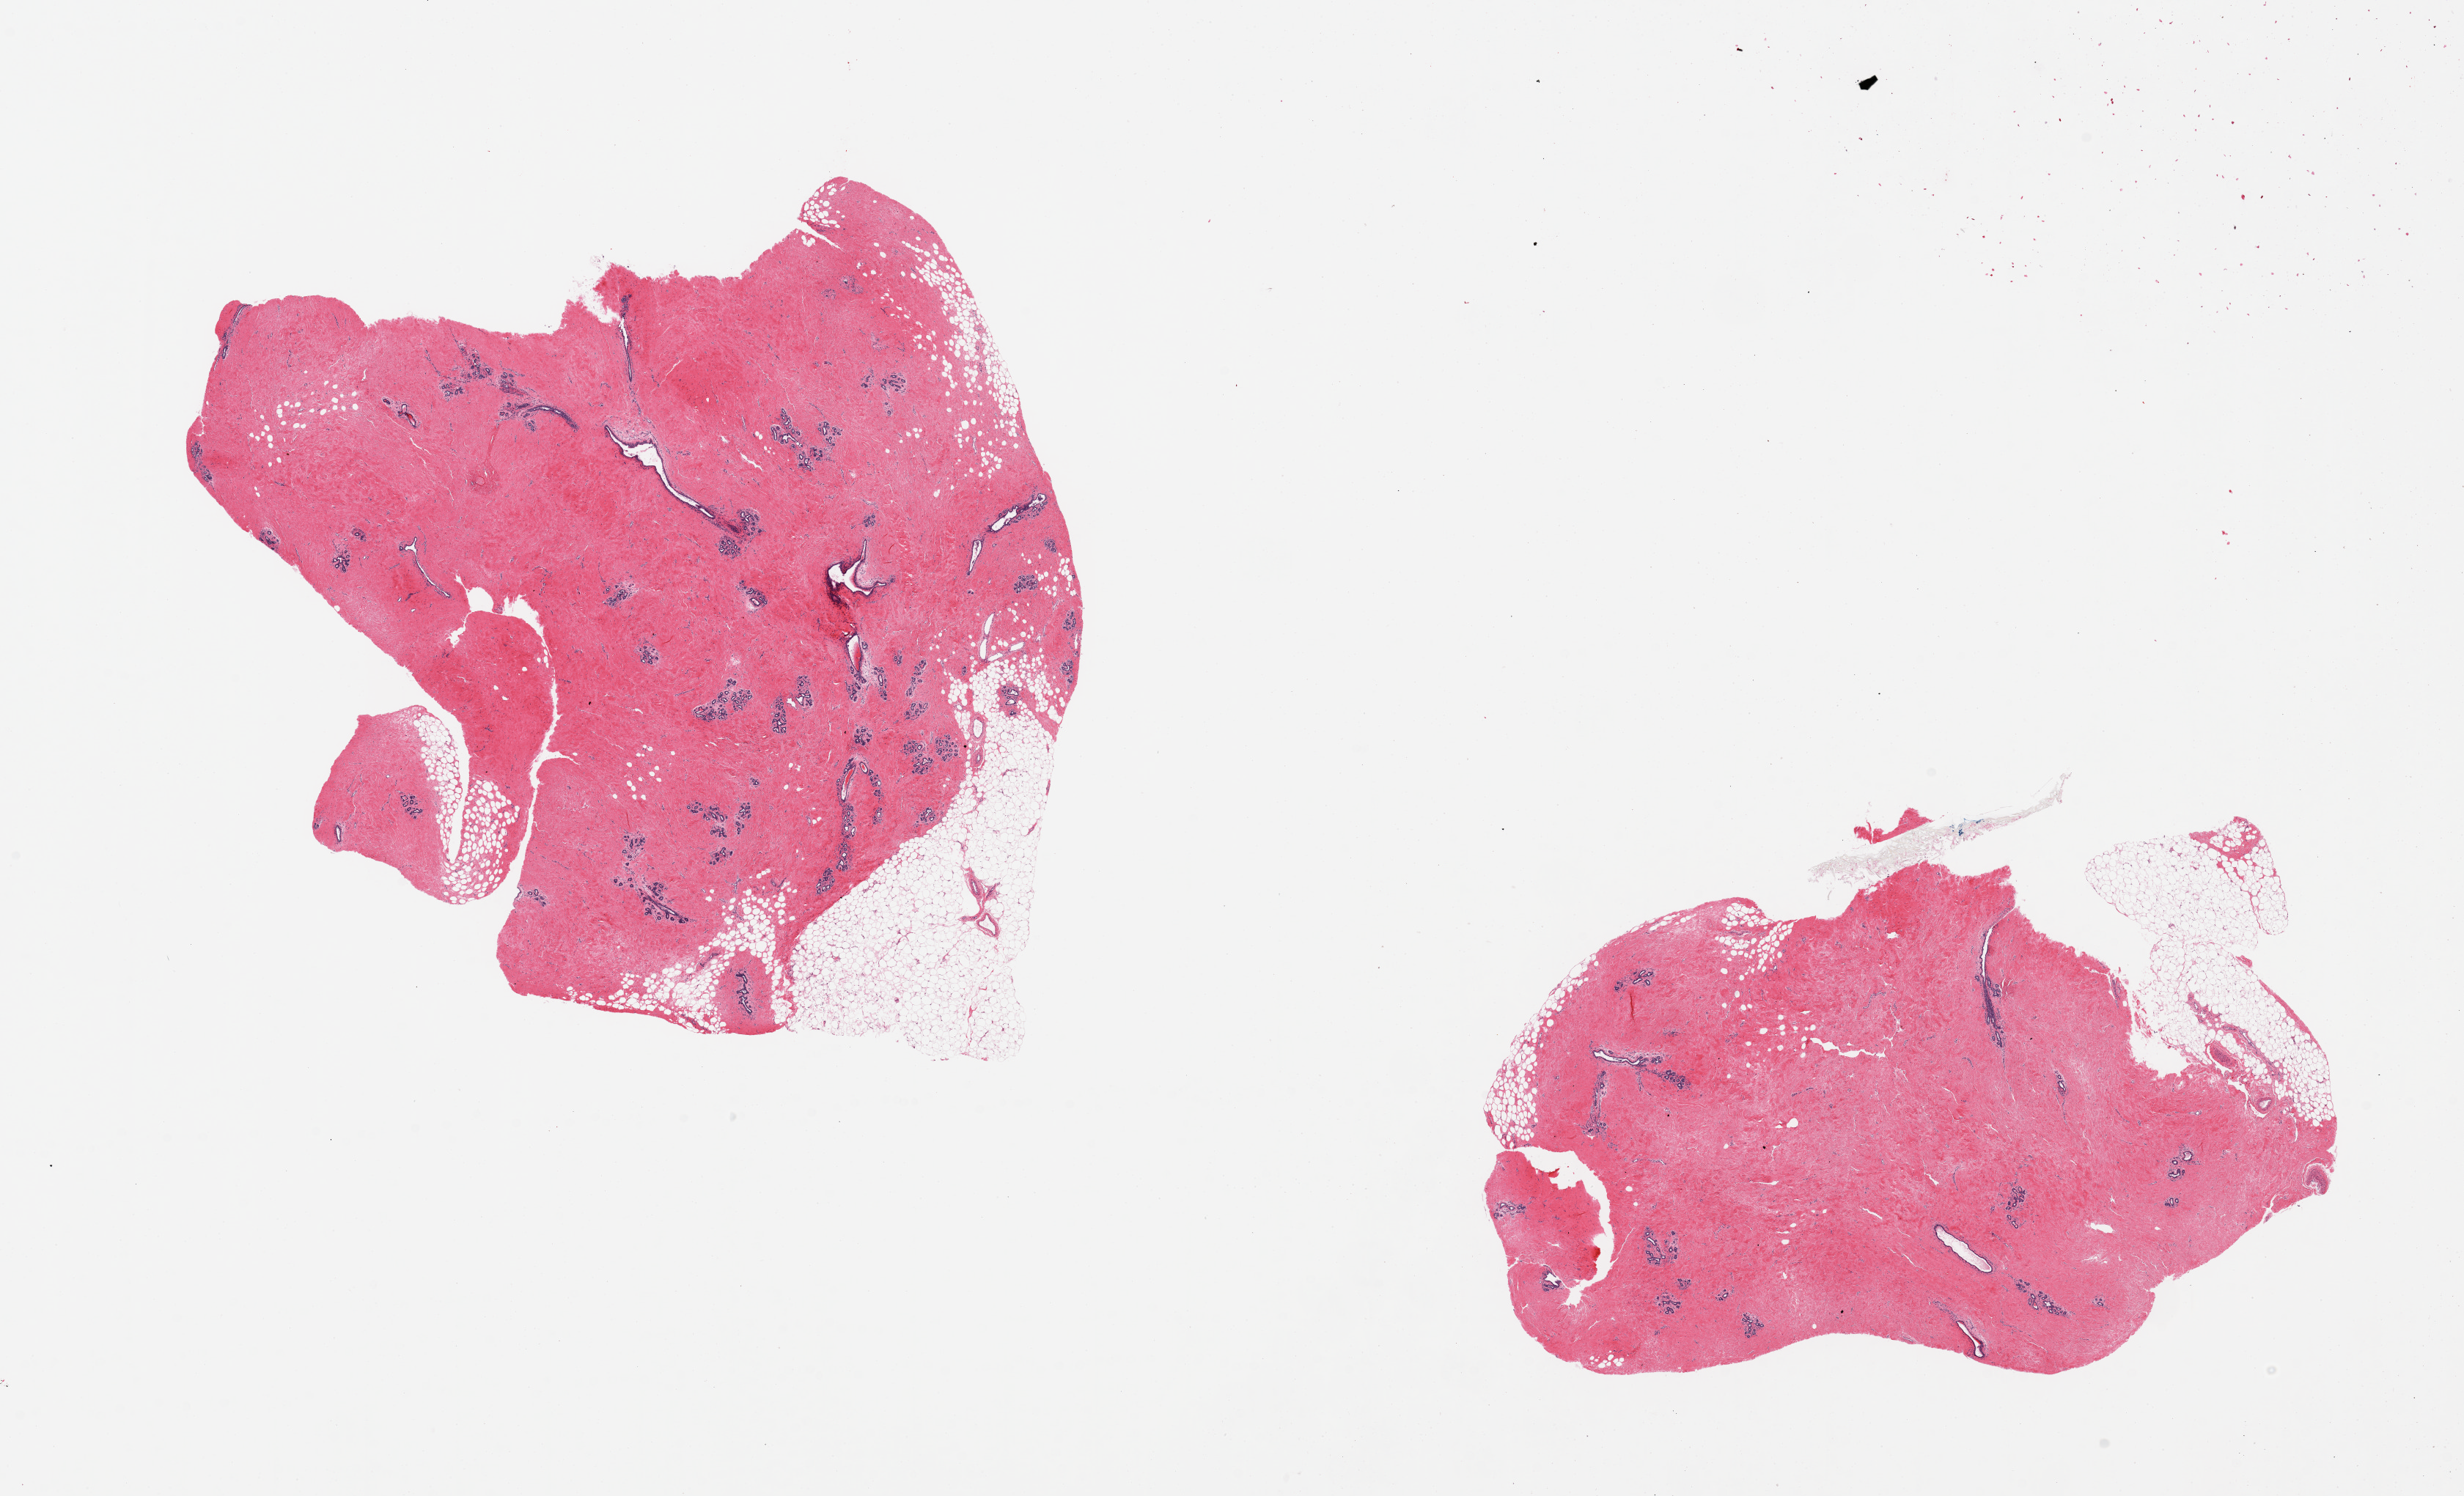
Whole-slide image, haematoxylin and eosin stain, whole scanned area (about 26.6 x 16.1 mm, acquisition: 20x scan) shown as a low-resolution overview. PAXgene-fixed, paraffin-embedded tissue. Target tissue: breast. Tissue donor sample. Male donor.
Reviewer comment on this tissue sample: 2 pieces, gynecomastoid hyperplasia.